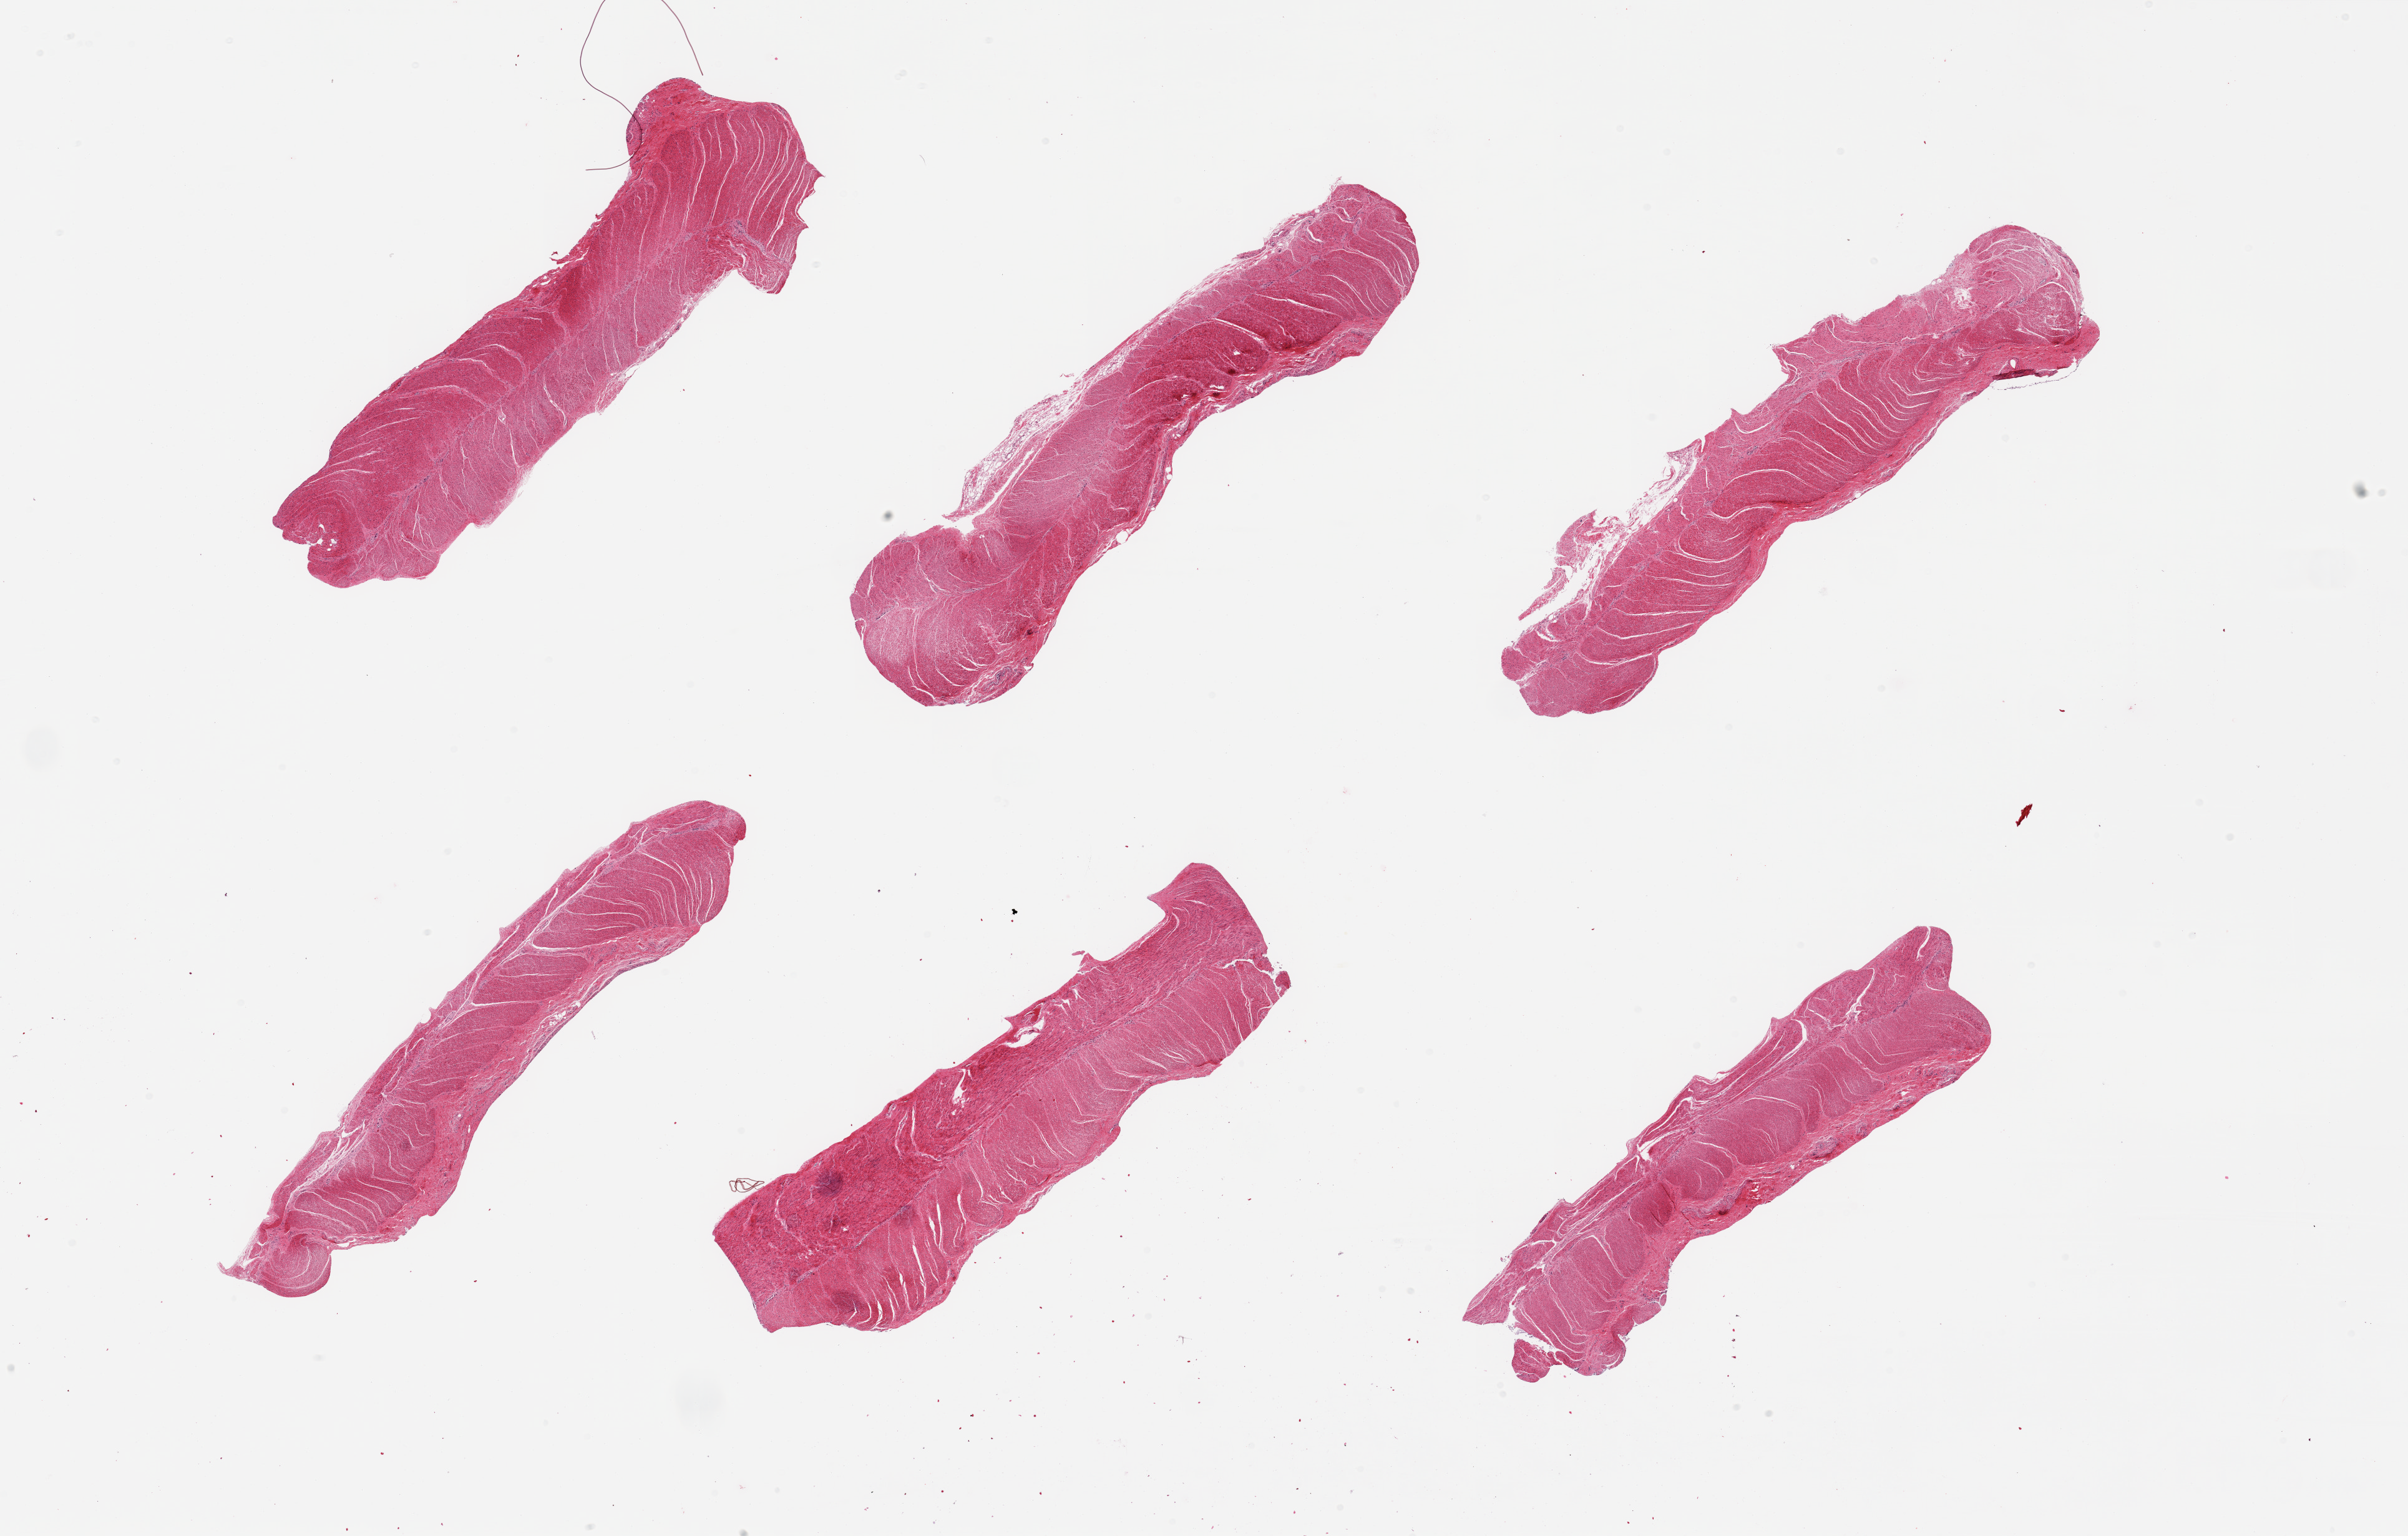
Digitized haematoxylin and eosin-stained section, a low-resolution overview of the entire scanned area, about 30.5 x 19.5 mm (acquisition: 20x scan); PAXgene-fixed, paraffin-embedded tissue; sampled site (target tissue): sigmoid colon; donor tissue sample. Donor: female.
Reviewer comment on this tissue sample: 6 pieces, target muscularis, unusually poorly preserved.